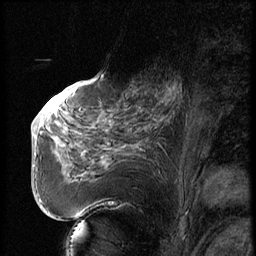
Breast MRI (dynamic contrast-enhanced), one sagittal slice; slice 32 of 74 in the series (ordered by position); dynamic contrast-enhanced series, image 2 of 3 at this slice position (ordered by acquisition); 1.5 T; TE 4.2 ms, TR 9 ms; 256 × 256 image matrix, field of view 180 × 180 mm. Patient: female, 56 years. From the clinical record (not read from this slice): setting: breast cancer imaged before/during neoadjuvant chemotherapy.
Outlined on this slice (semi-automatically segmented with operator editing):
- analysis volume of interest (the breast-tissue region the enhancement analysis was run in; not a lesion): bounding box [x1, y1, x2, y2] px = [123, 71, 195, 131]
- tumour enhancement mask (voxels above the 140 % enhancement threshold inside the analysis volume of interest): [159, 84, 181, 106]